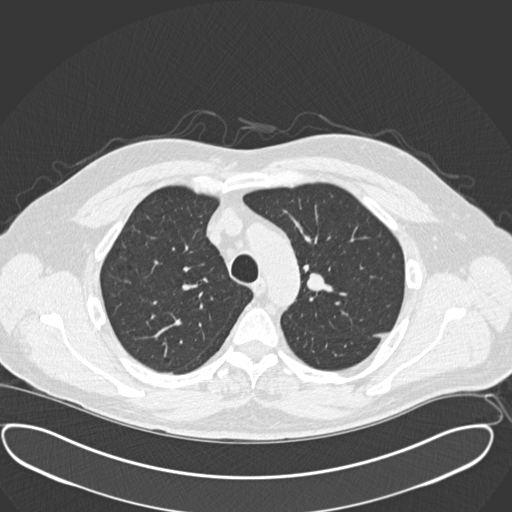
Chest CT (low-dose screening protocol), one axial image, third annual screen, lung window (W 1500 / L -600 HU), 2 mm slice thickness, standard (soft-tissue) reconstruction kernel (B30f), 120 kVp, slice 47 of 181 in the series, 512 × 512 image matrix. Male, age 56 years at enrolment.
- Lesion marked by an expert reader, bounding box (x1, y1, x2, y2) in pixels: (288, 262, 343, 309).
- No non-calcified nodule or mass ≥4 mm was recorded by the screening reader at this exam.
- Lung cancer was diagnosed 156 days after this screen: neuroendocrine carcinoma, NOS, left upper lobe, well differentiated (G1), stage IA (AJCC 6th edition), 20 mm at pathology.